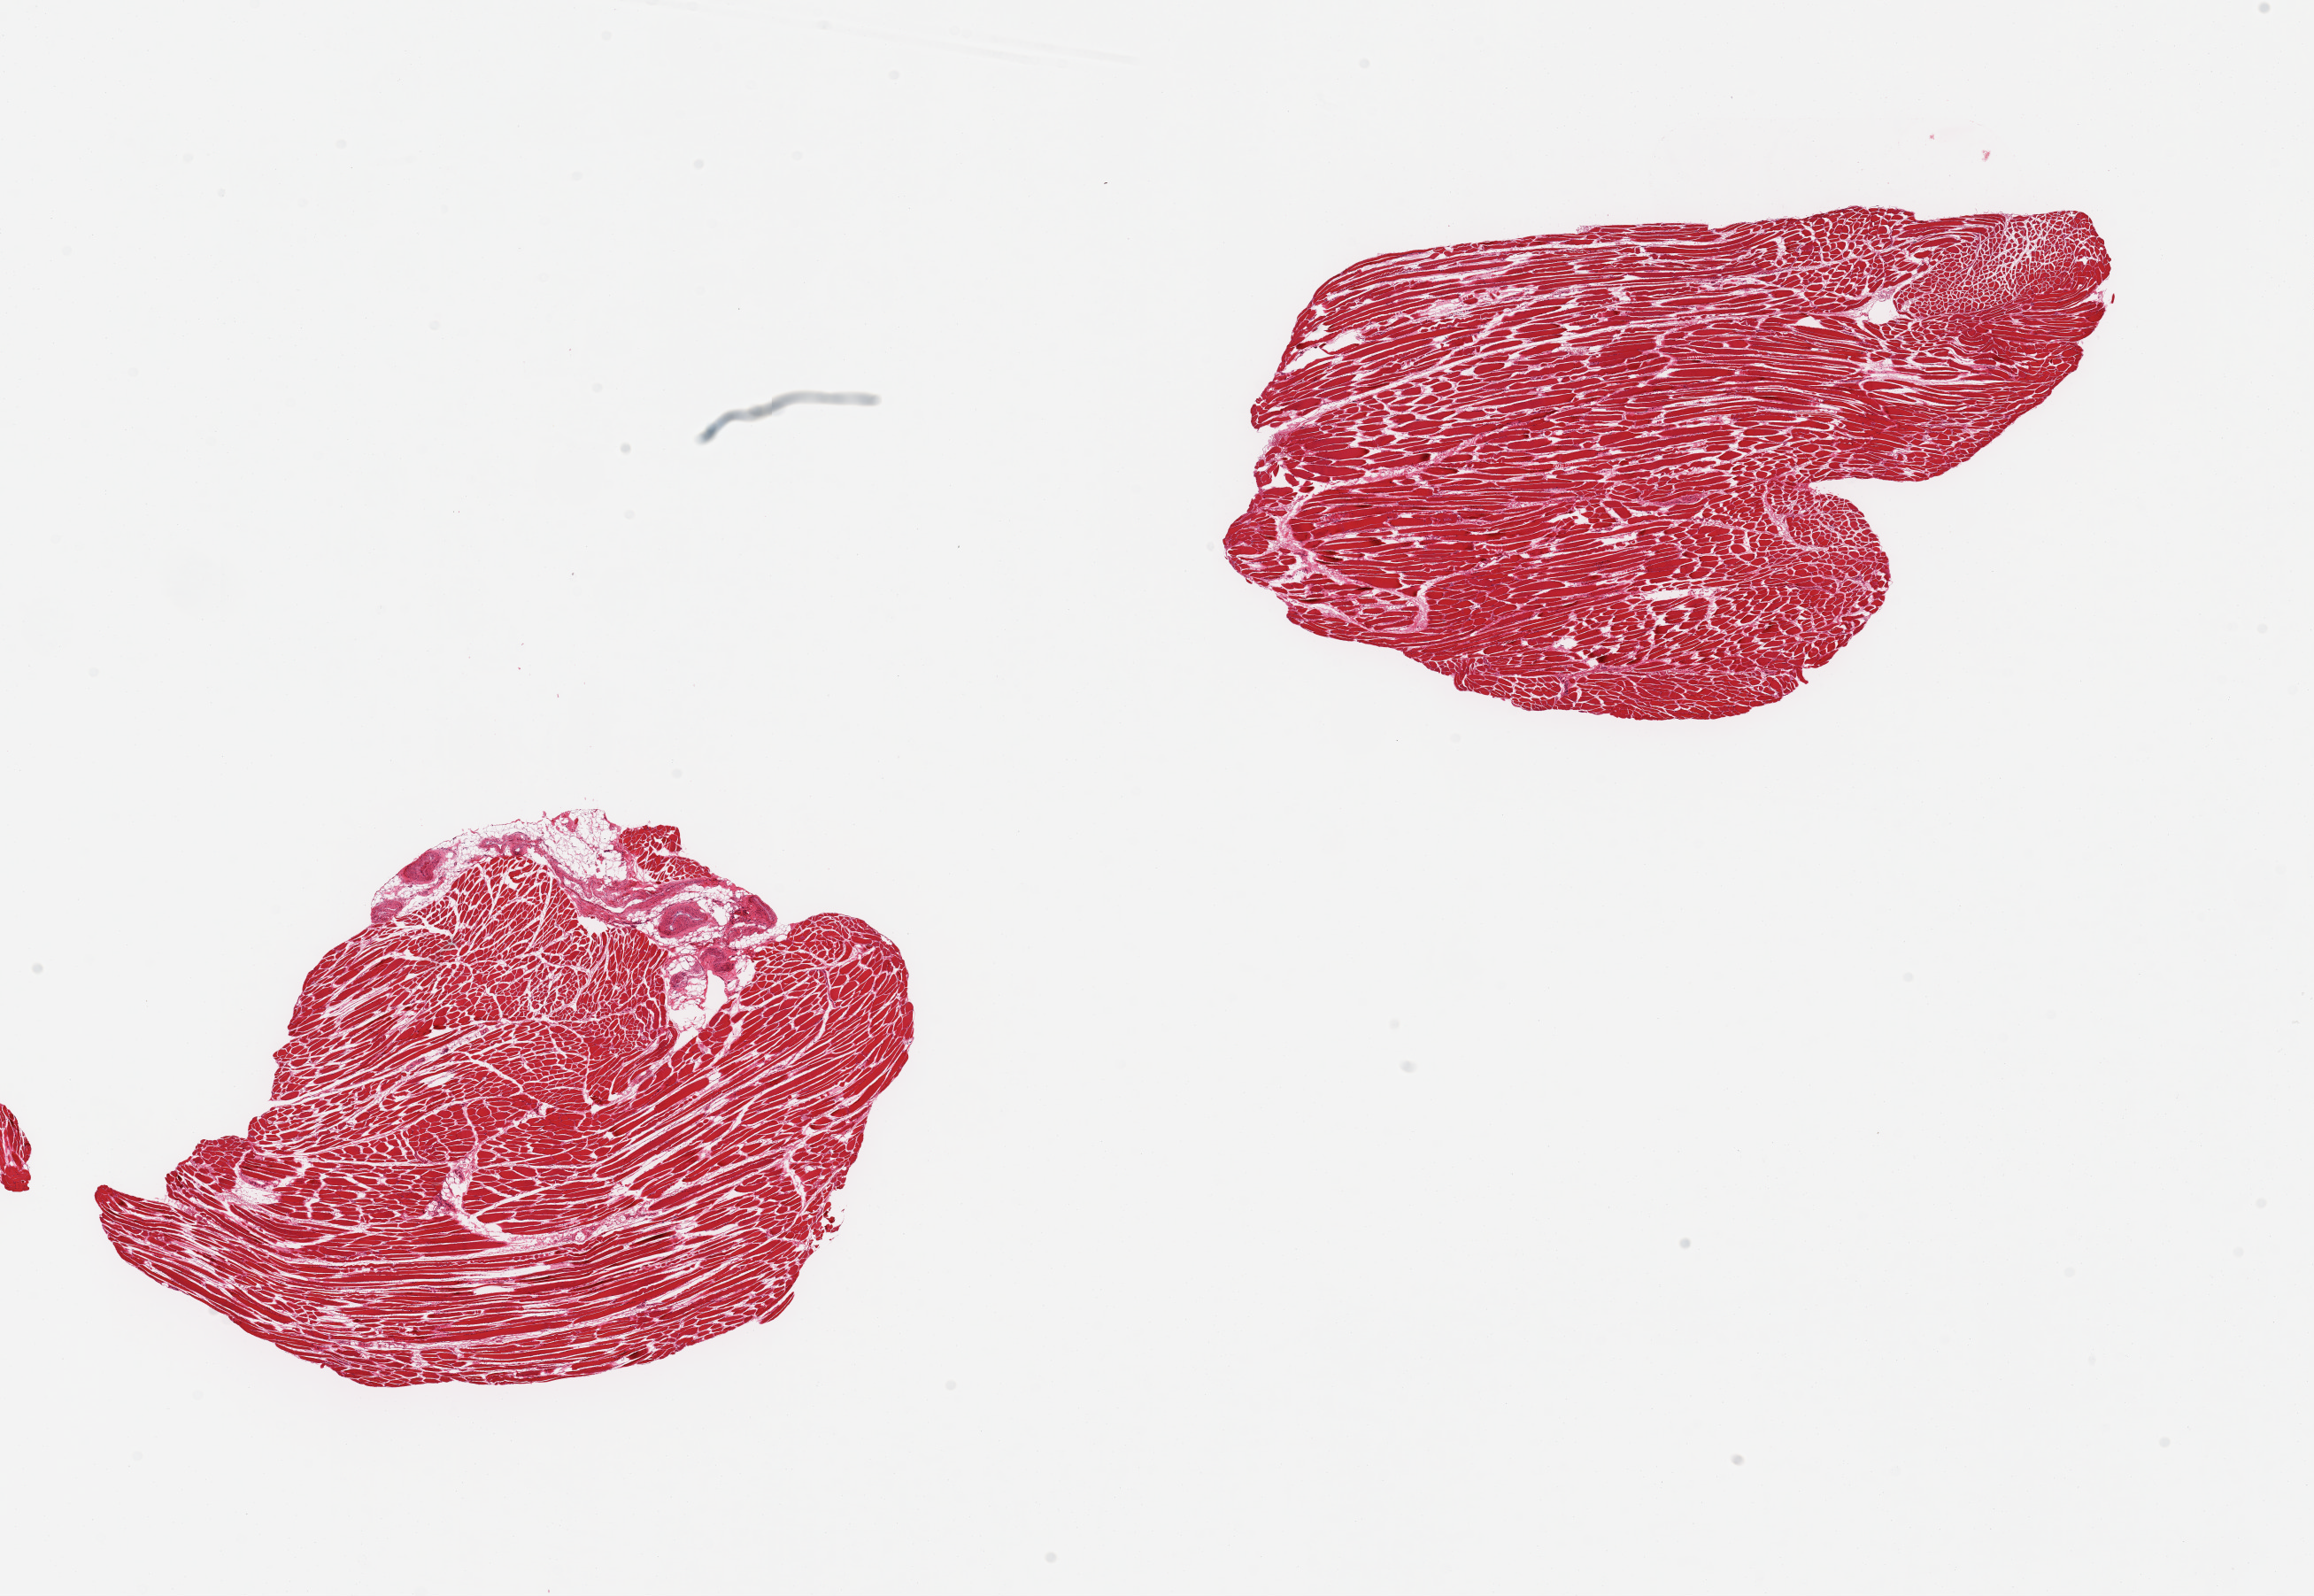
Whole-slide image, hematoxylin and eosin (H&E) stain, brightfield — whole scanned area (about 20.7 x 14.3 mm) shown as a low-resolution overview, PAXgene-fixed paraffin-embedded (PFPE) section, section of skeletal muscle (target tissue), tissue donor sample. Female donor.
Review note (as recorded): 2 pieces; 5% internal fat.